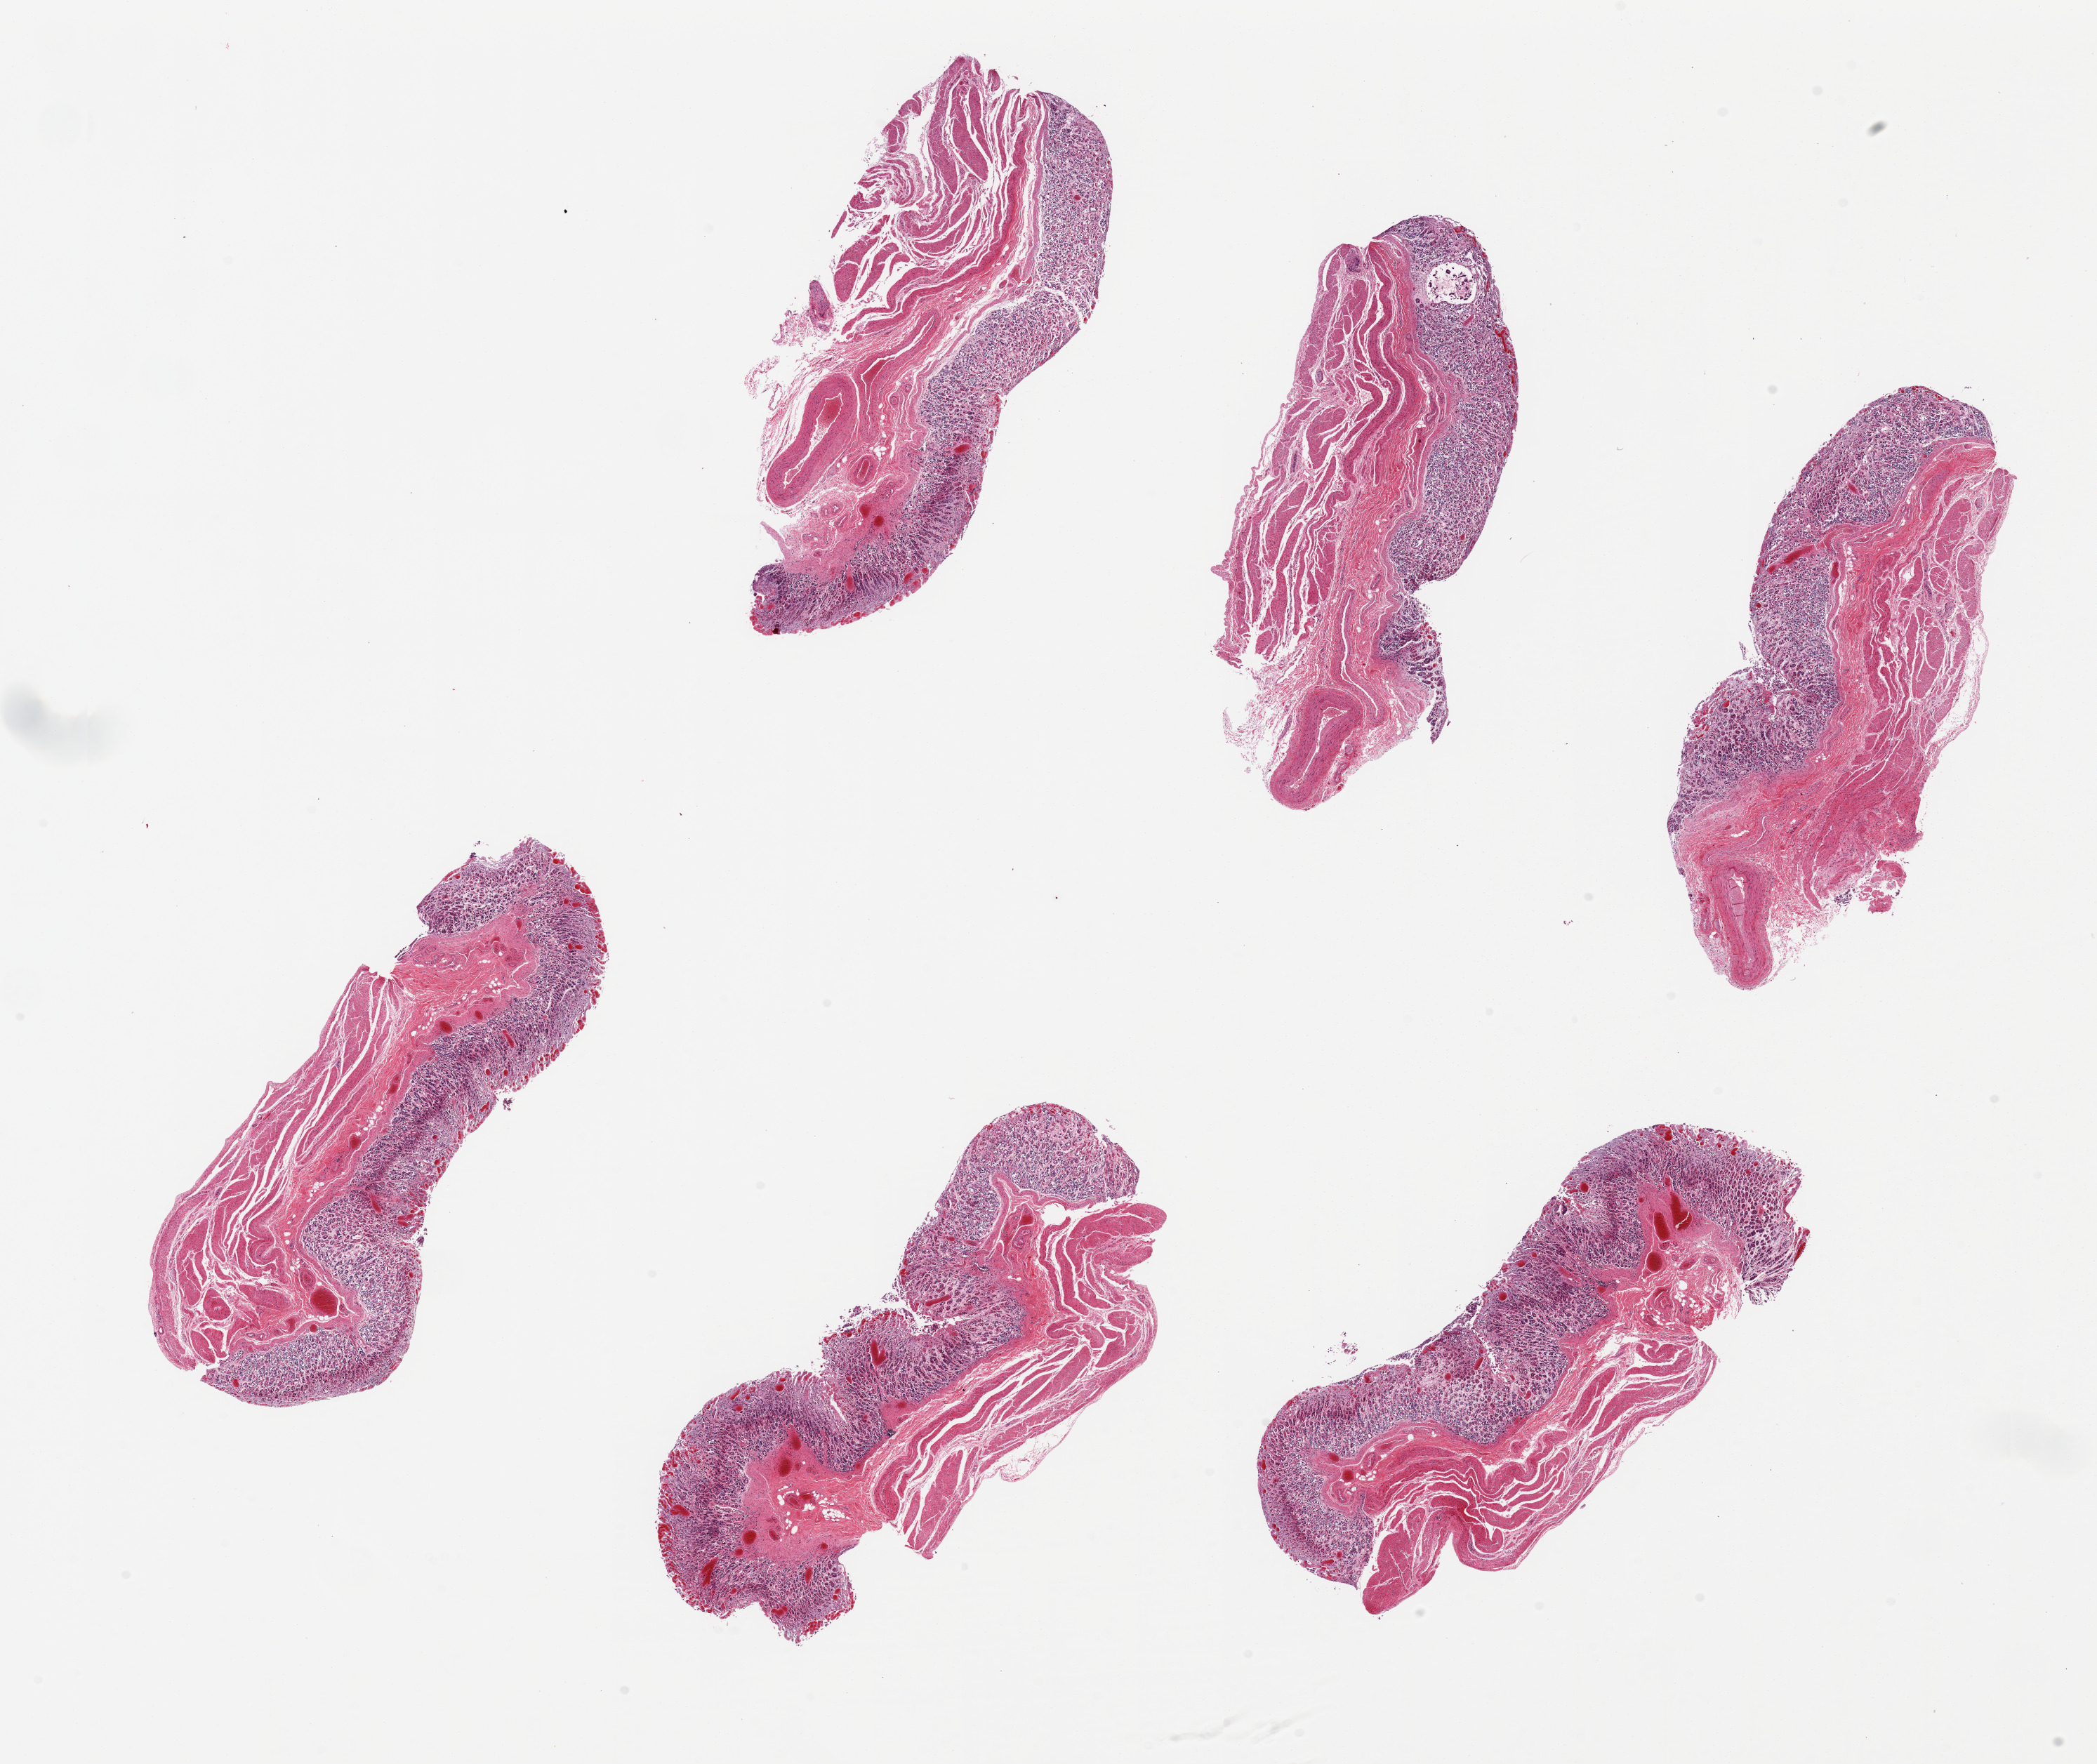
Digitized haematoxylin and eosin-stained section, brightfield, a low-resolution overview of the entire scanned area, about 23.6 x 19.9 mm (from a 20x scan). PAXgene-fixed paraffin-embedded (PFPE) section. Target tissue: stomach. Donor tissue sample. Donor: male.
Pathologist's review note for this sample: 6 pieces, up to 7x3mm; mucosa=3; muscle =2 (autolysis).